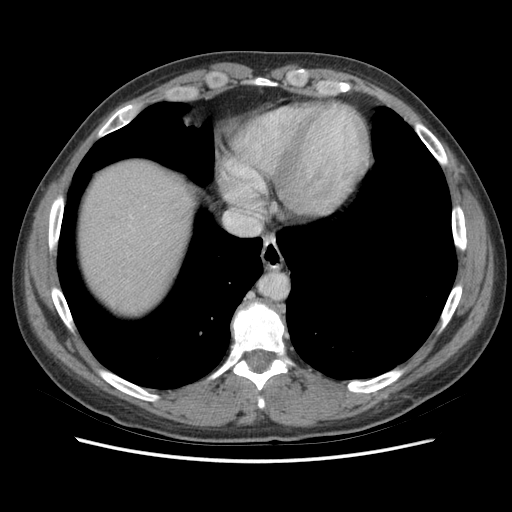
Contrast-enhanced abdominal CT (liver protocol), one axial slice. Soft-tissue window (W 400 / L 40 HU). 2.5 mm slice thickness. 512 × 512 image matrix, field of view 360 × 360 mm. Case-level facts recorded for this patient, not image findings: diagnosis: hepatocellular carcinoma (patient treated with transarterial chemoembolisation; whether this scan precedes or follows treatment is not stated here); TNM stage (as recorded): Stage-IIIA; Child-Pugh class: A; tumour nodularity: multinodular.
Annotated regions visible in this slice (semi-automatically segmented with operator editing):
- abdominal aorta: bounding box (x1, y1, x2, y2) in pixels: (261, 275, 288, 299)
- liver parenchyma outside the tumour (the mass and vessels are separate outlines, so this box may not span the whole liver): (80, 160, 192, 312)